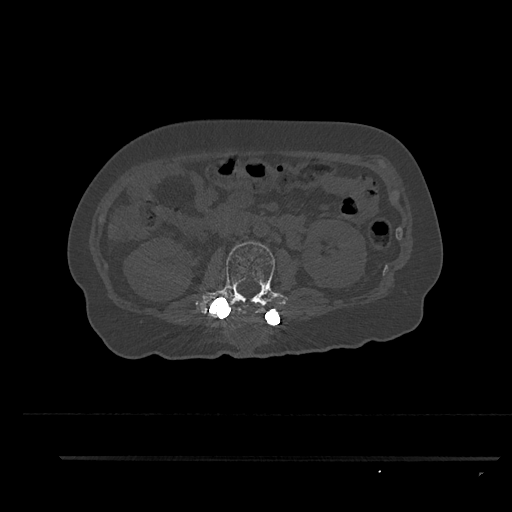
CT including the spine, one axial slice. Reconstruction kernel Br40s/3. 120 kVp. Bone window (W 1800 / L 400 HU). 512 × 512 image matrix. Patient: female, 44 years. From the clinical record (not read from this slice): primary cancer: renal; vertebrae with lytic lesions (as recorded): L1.
Structures marked on this image (semi-automatically segmented with operator editing):
- L2 vertebra: bounding box (x1, y1, x2, y2) in pixels: (195, 241, 284, 320)